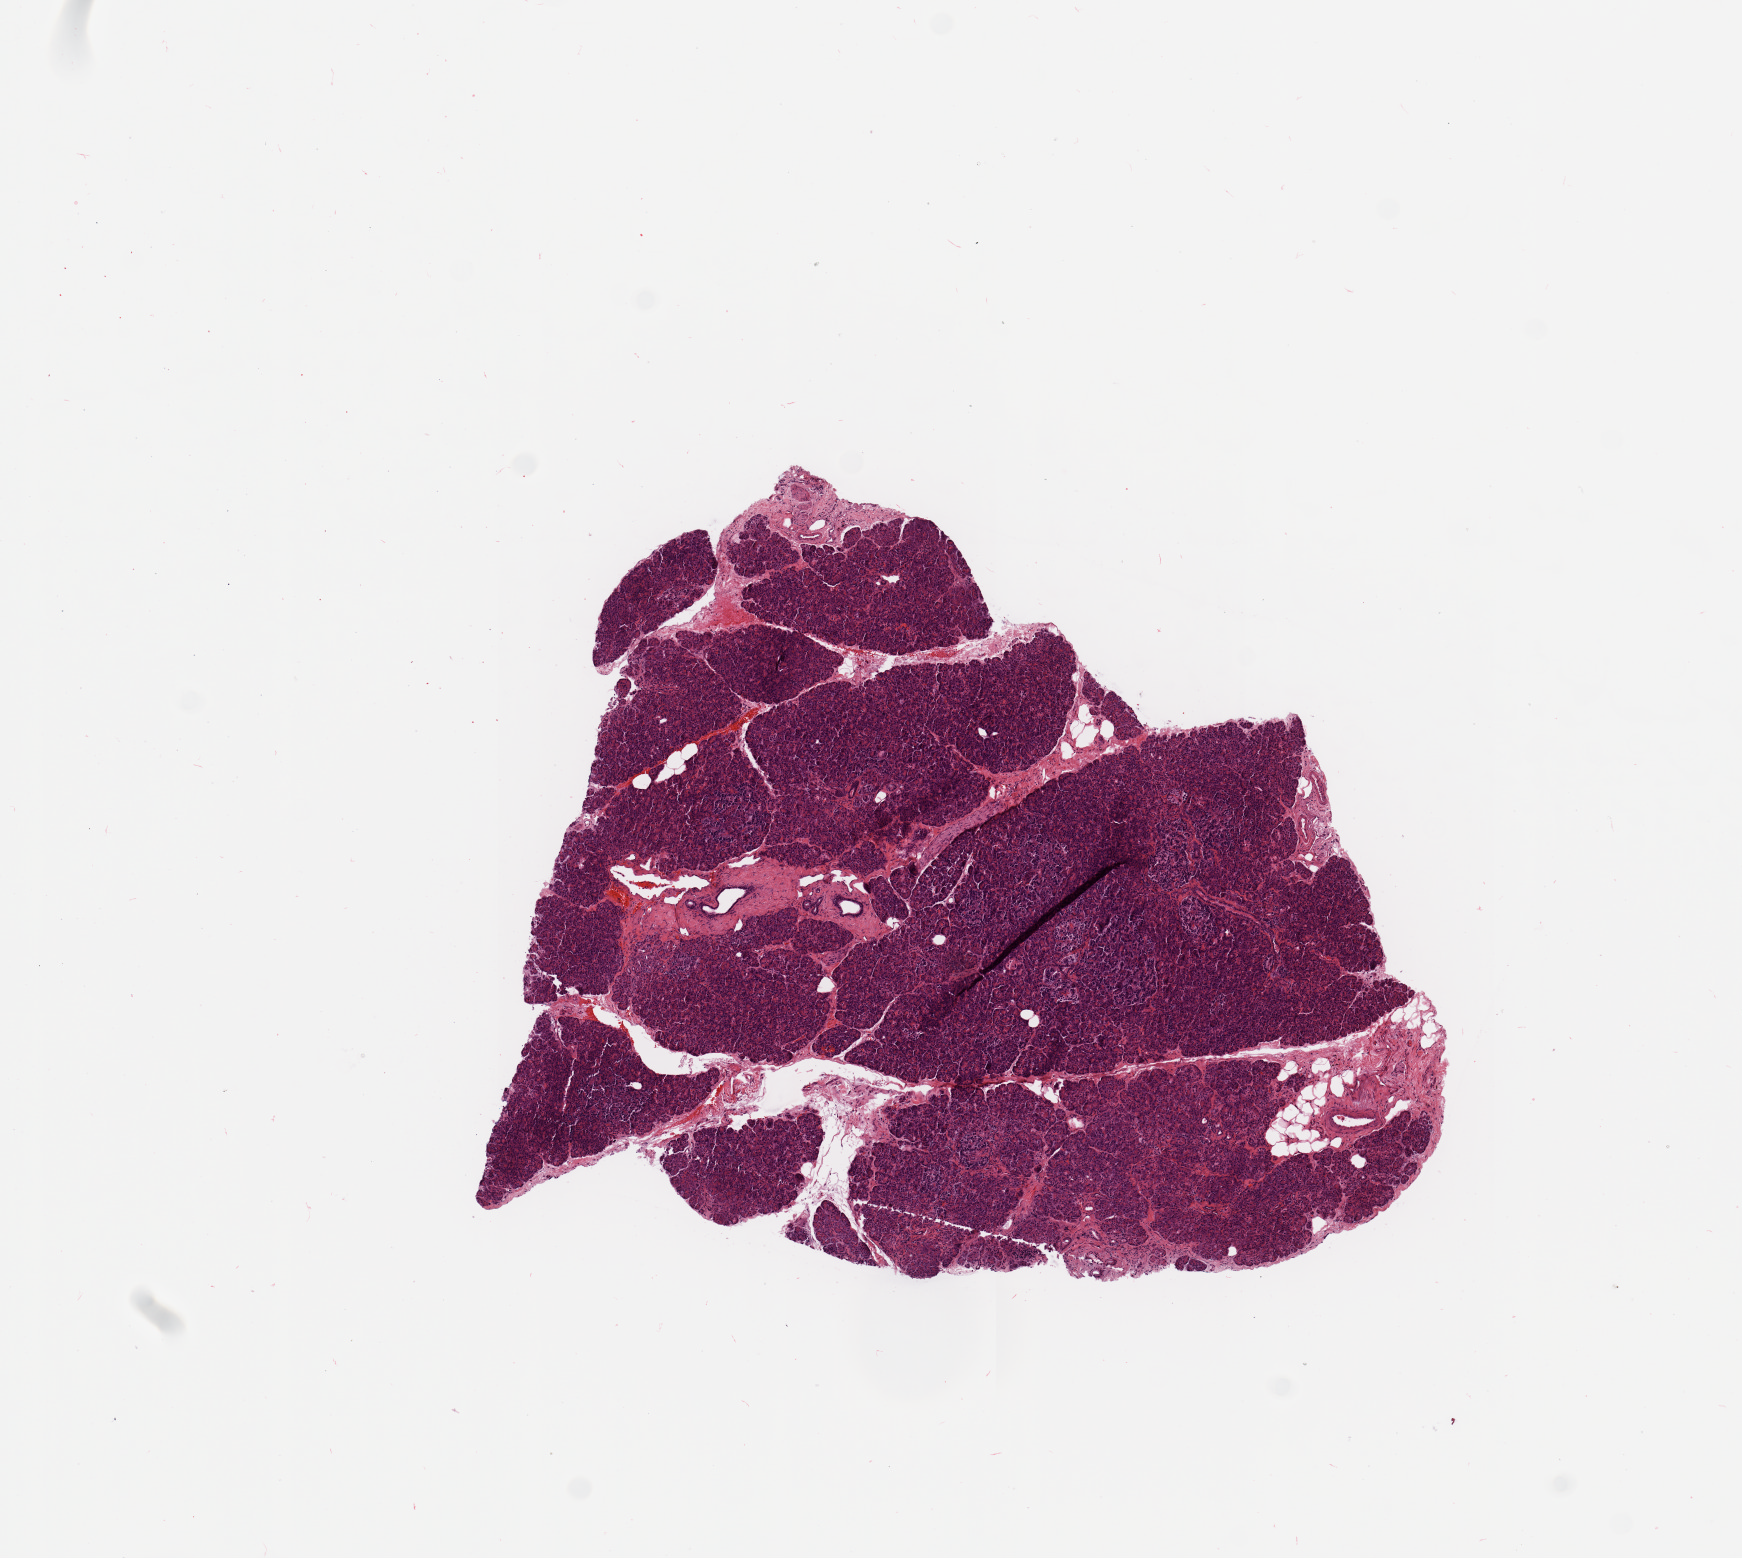
Whole-slide histology image, H&E-stained — whole scanned area (about 6.9 x 6.2 mm) shown as a low-resolution overview; pancreas, normal (non-tumour) tissue. Male, 66 y/o.
This section: normal (non-tumour) tissue from the same patient. Patient diagnosis: Infiltrating duct carcinoma, NOS.